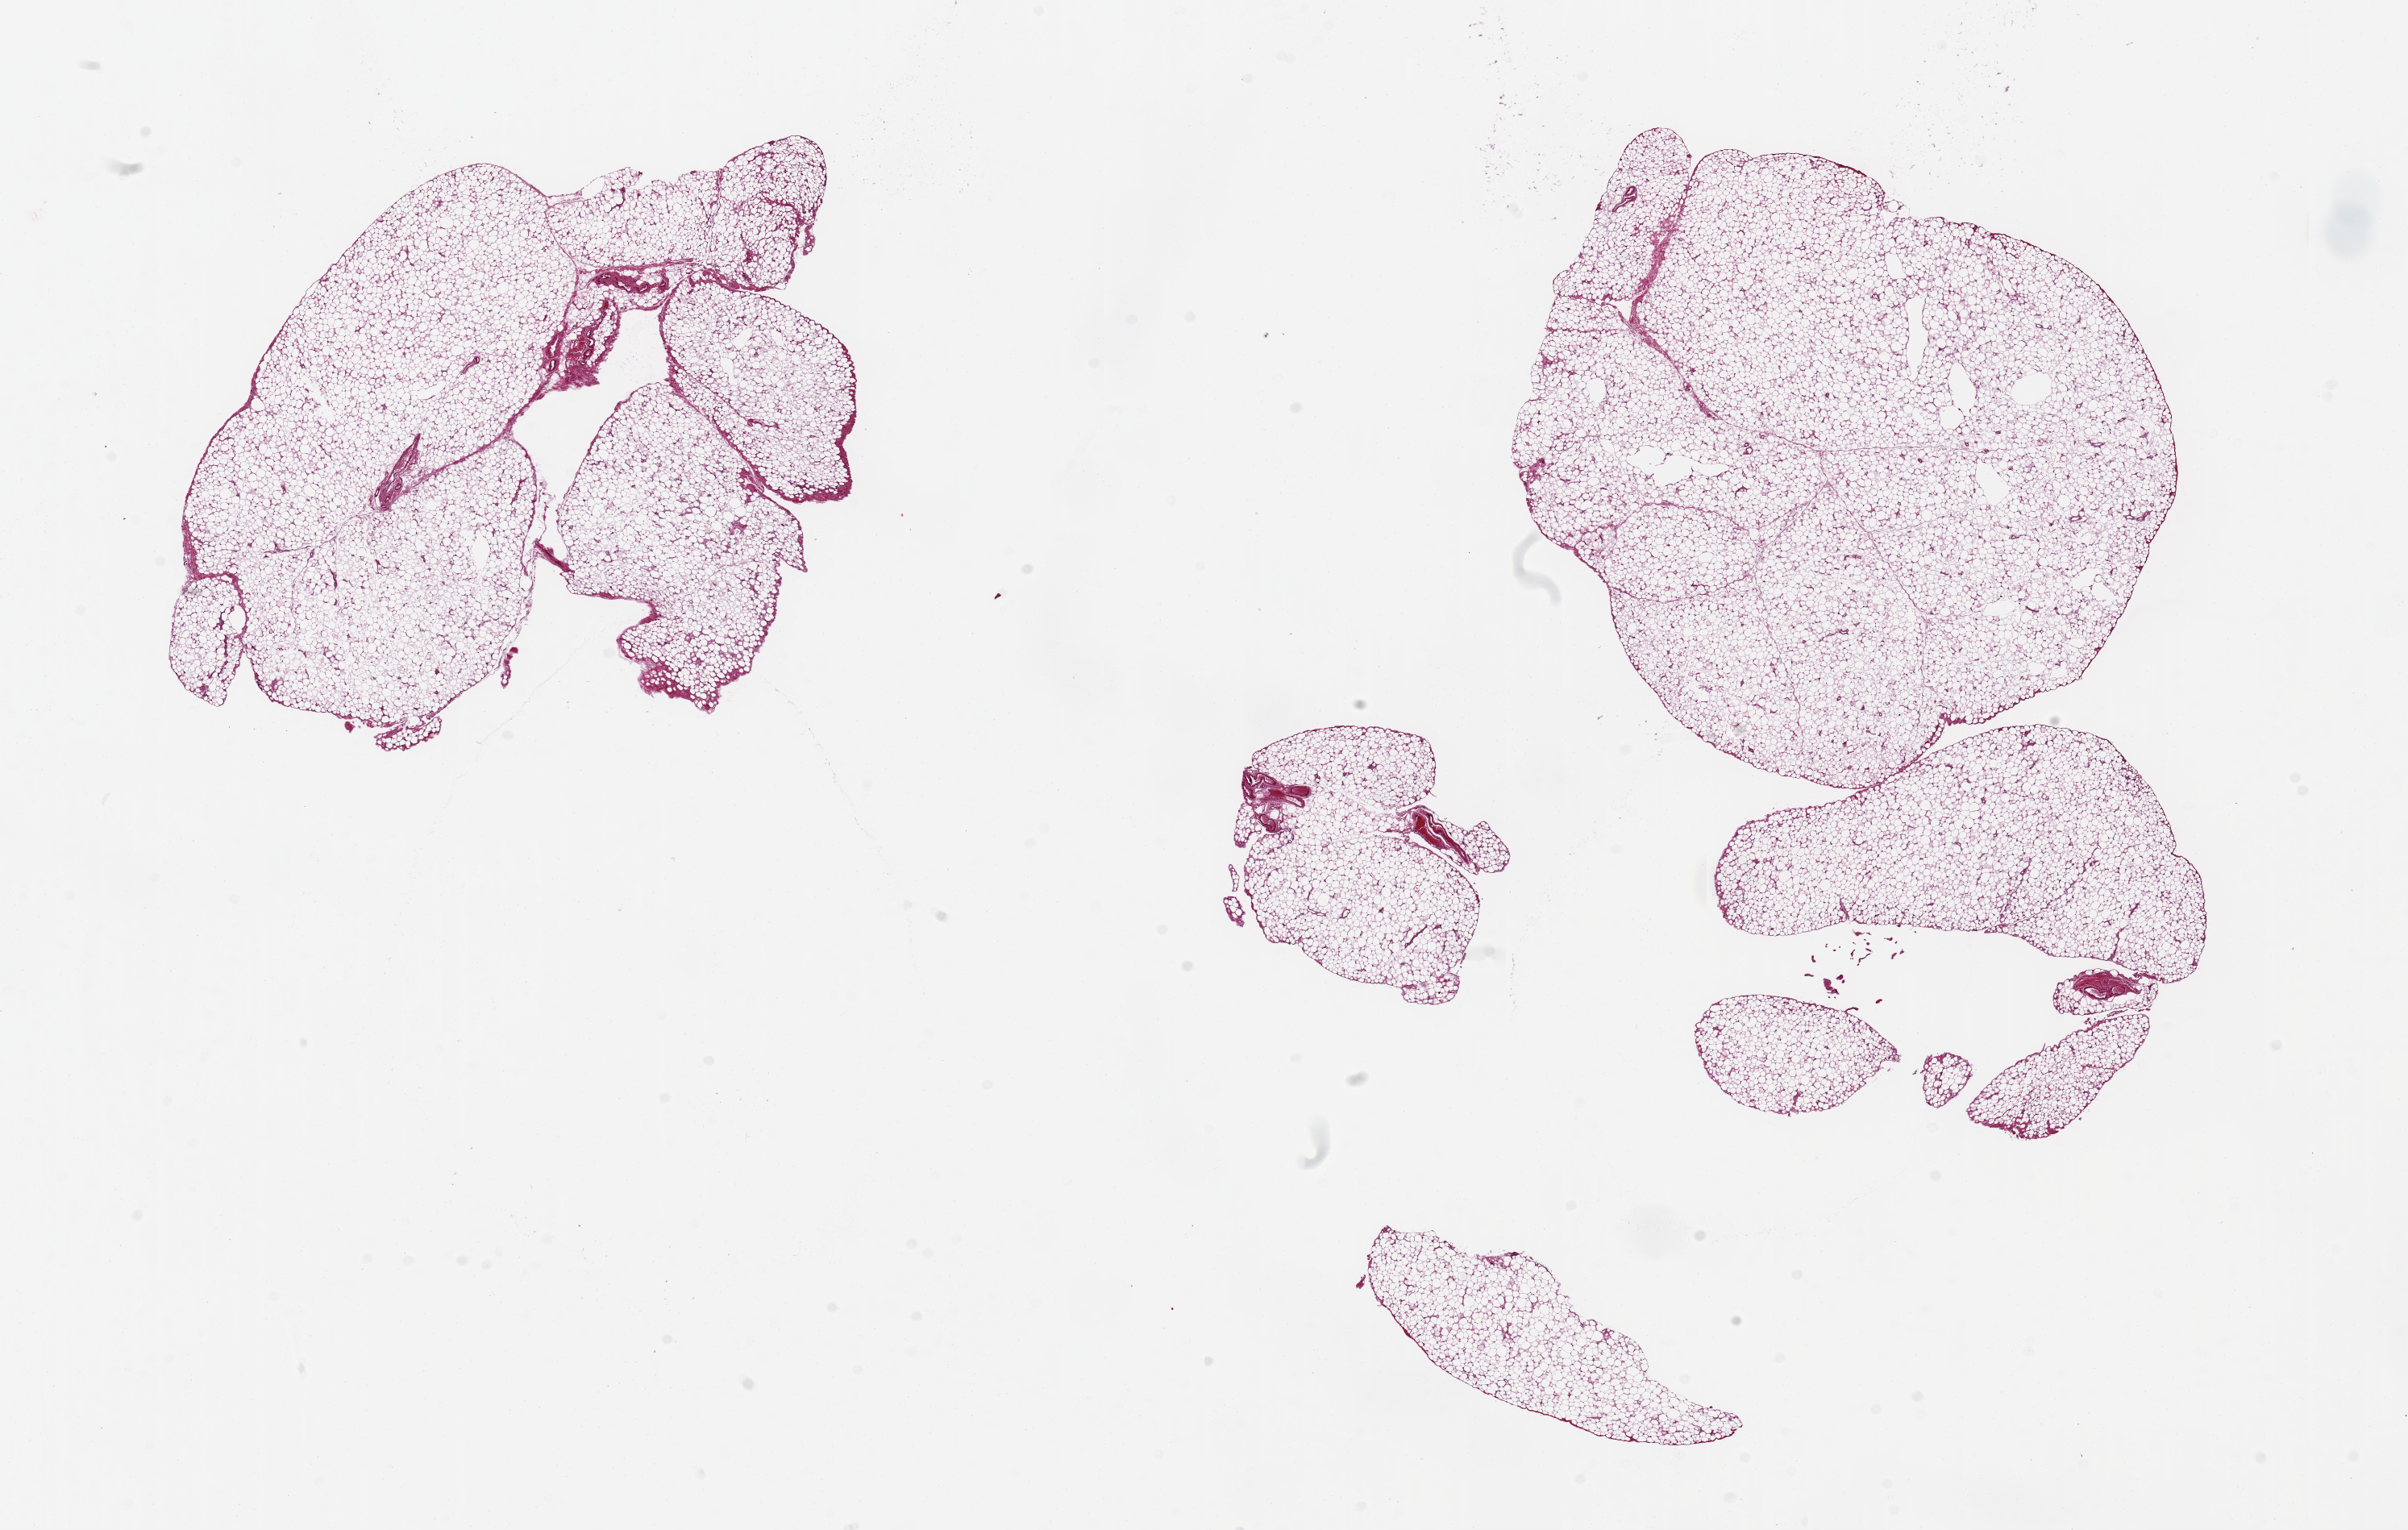
H&E whole-slide image, brightfield, shown as a low-resolution overview of the whole scanned area (about 23.6 x 15.0 mm); PAXgene-fixed paraffin-embedded (PFPE) section; target tissue: omentum; tissue donor sample. Donor: female.
Review note (as recorded): 2 pieces, 8x6 & 11x6mm.